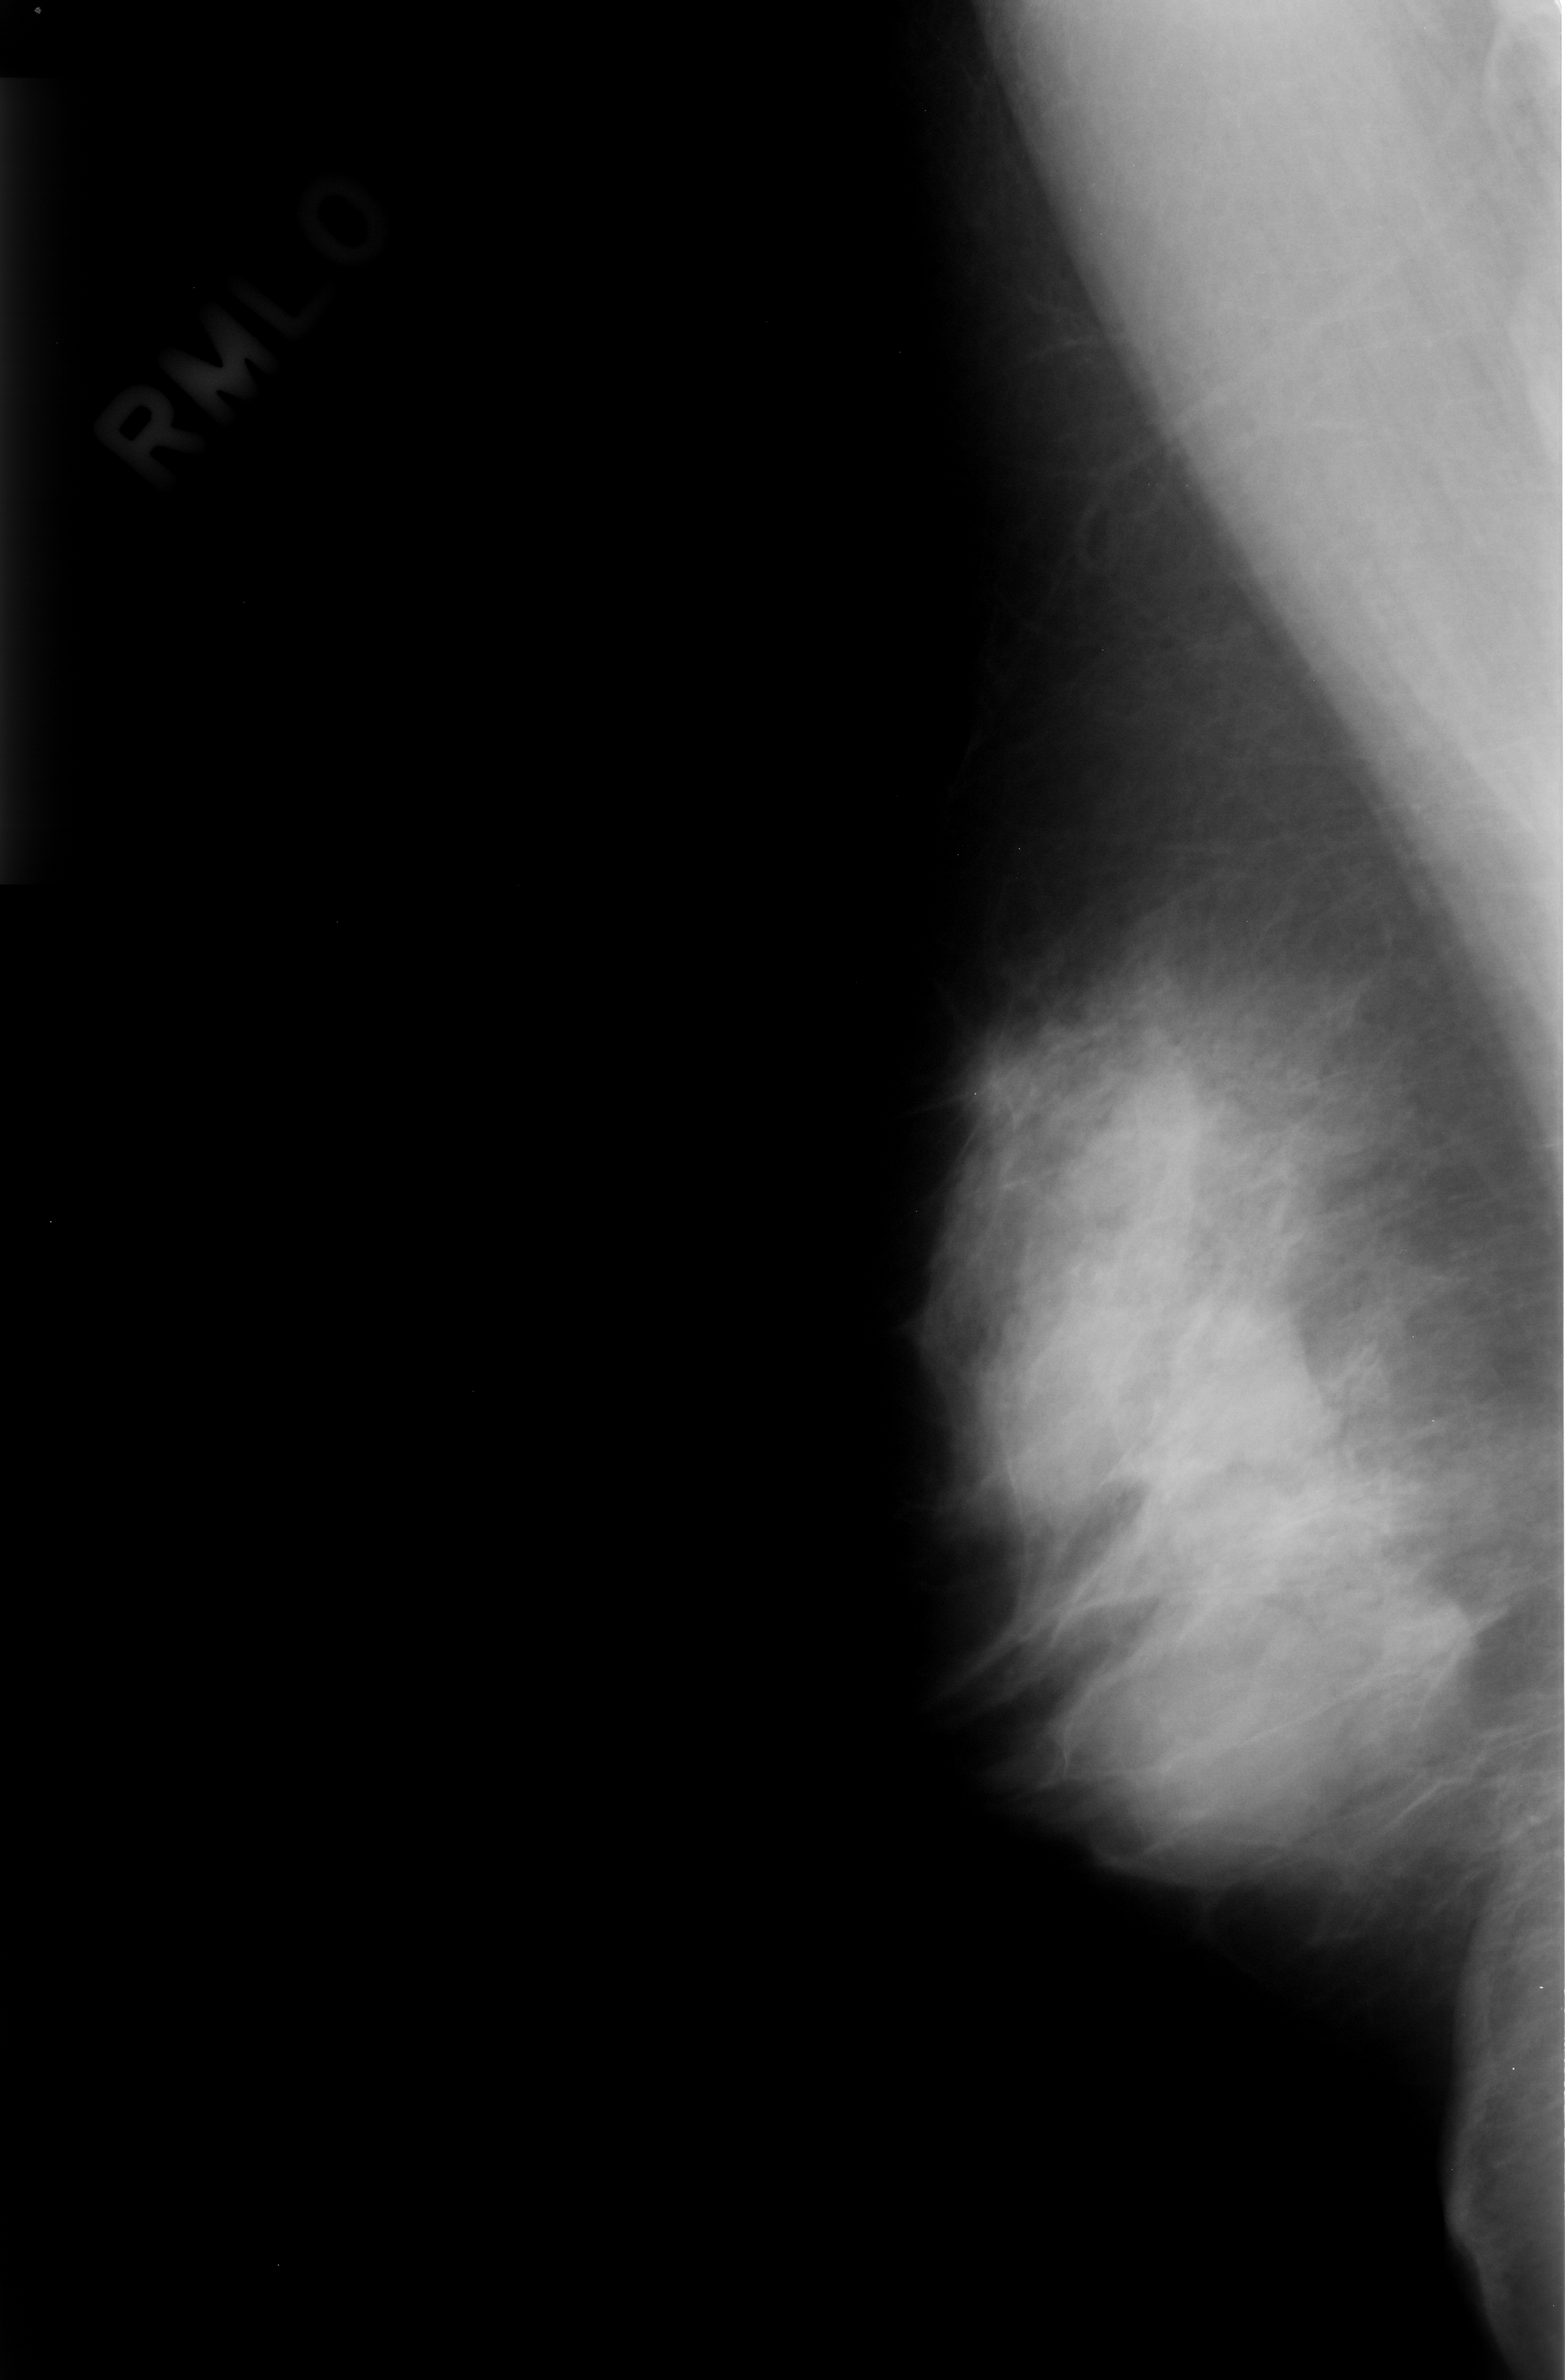
Digitized screen-film mammogram, right breast, mediolateral oblique (MLO) view, BI-RADS breast density category 4 (scale 1–4).
Finding: mass, shape lobulated, margins obscured; BI-RADS assessment category 3; subtlety rating 4 on a 1 (subtle) to 5 (obvious) scale; pathology result (as recorded, not read from the image): benign.